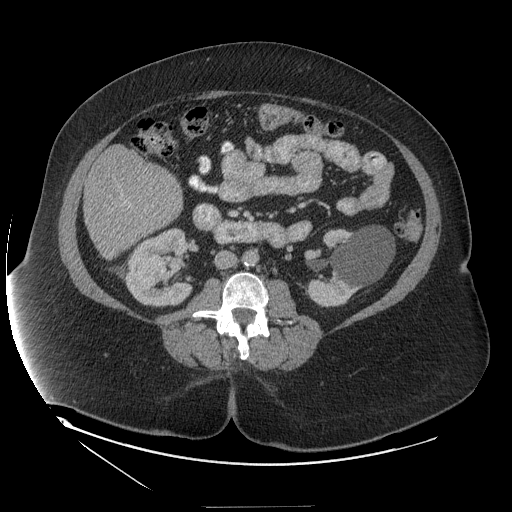
Contrast-enhanced abdominal CT (liver protocol), one axial slice; slice 40 of 127 in the series (ordered by position); 140 kVp; soft-tissue window (W 400 / L 40 HU); 512 × 512 image matrix, field of view 480 × 480 mm. Case-level facts recorded for this patient, not image findings: diagnosis: hepatocellular carcinoma (patient treated with transarterial chemoembolisation; whether this scan precedes or follows treatment is not stated here); TNM stage (as recorded): Stage-II; Child-Pugh class: A; tumour size: 3 cm.
Annotated regions visible in this slice (semi-automatically segmented with operator editing):
- liver parenchyma outside the tumour (the mass and vessels are separate outlines, so this box may not span the whole liver): bounding box (x1, y1, x2, y2) in pixels: (84, 148, 182, 258)